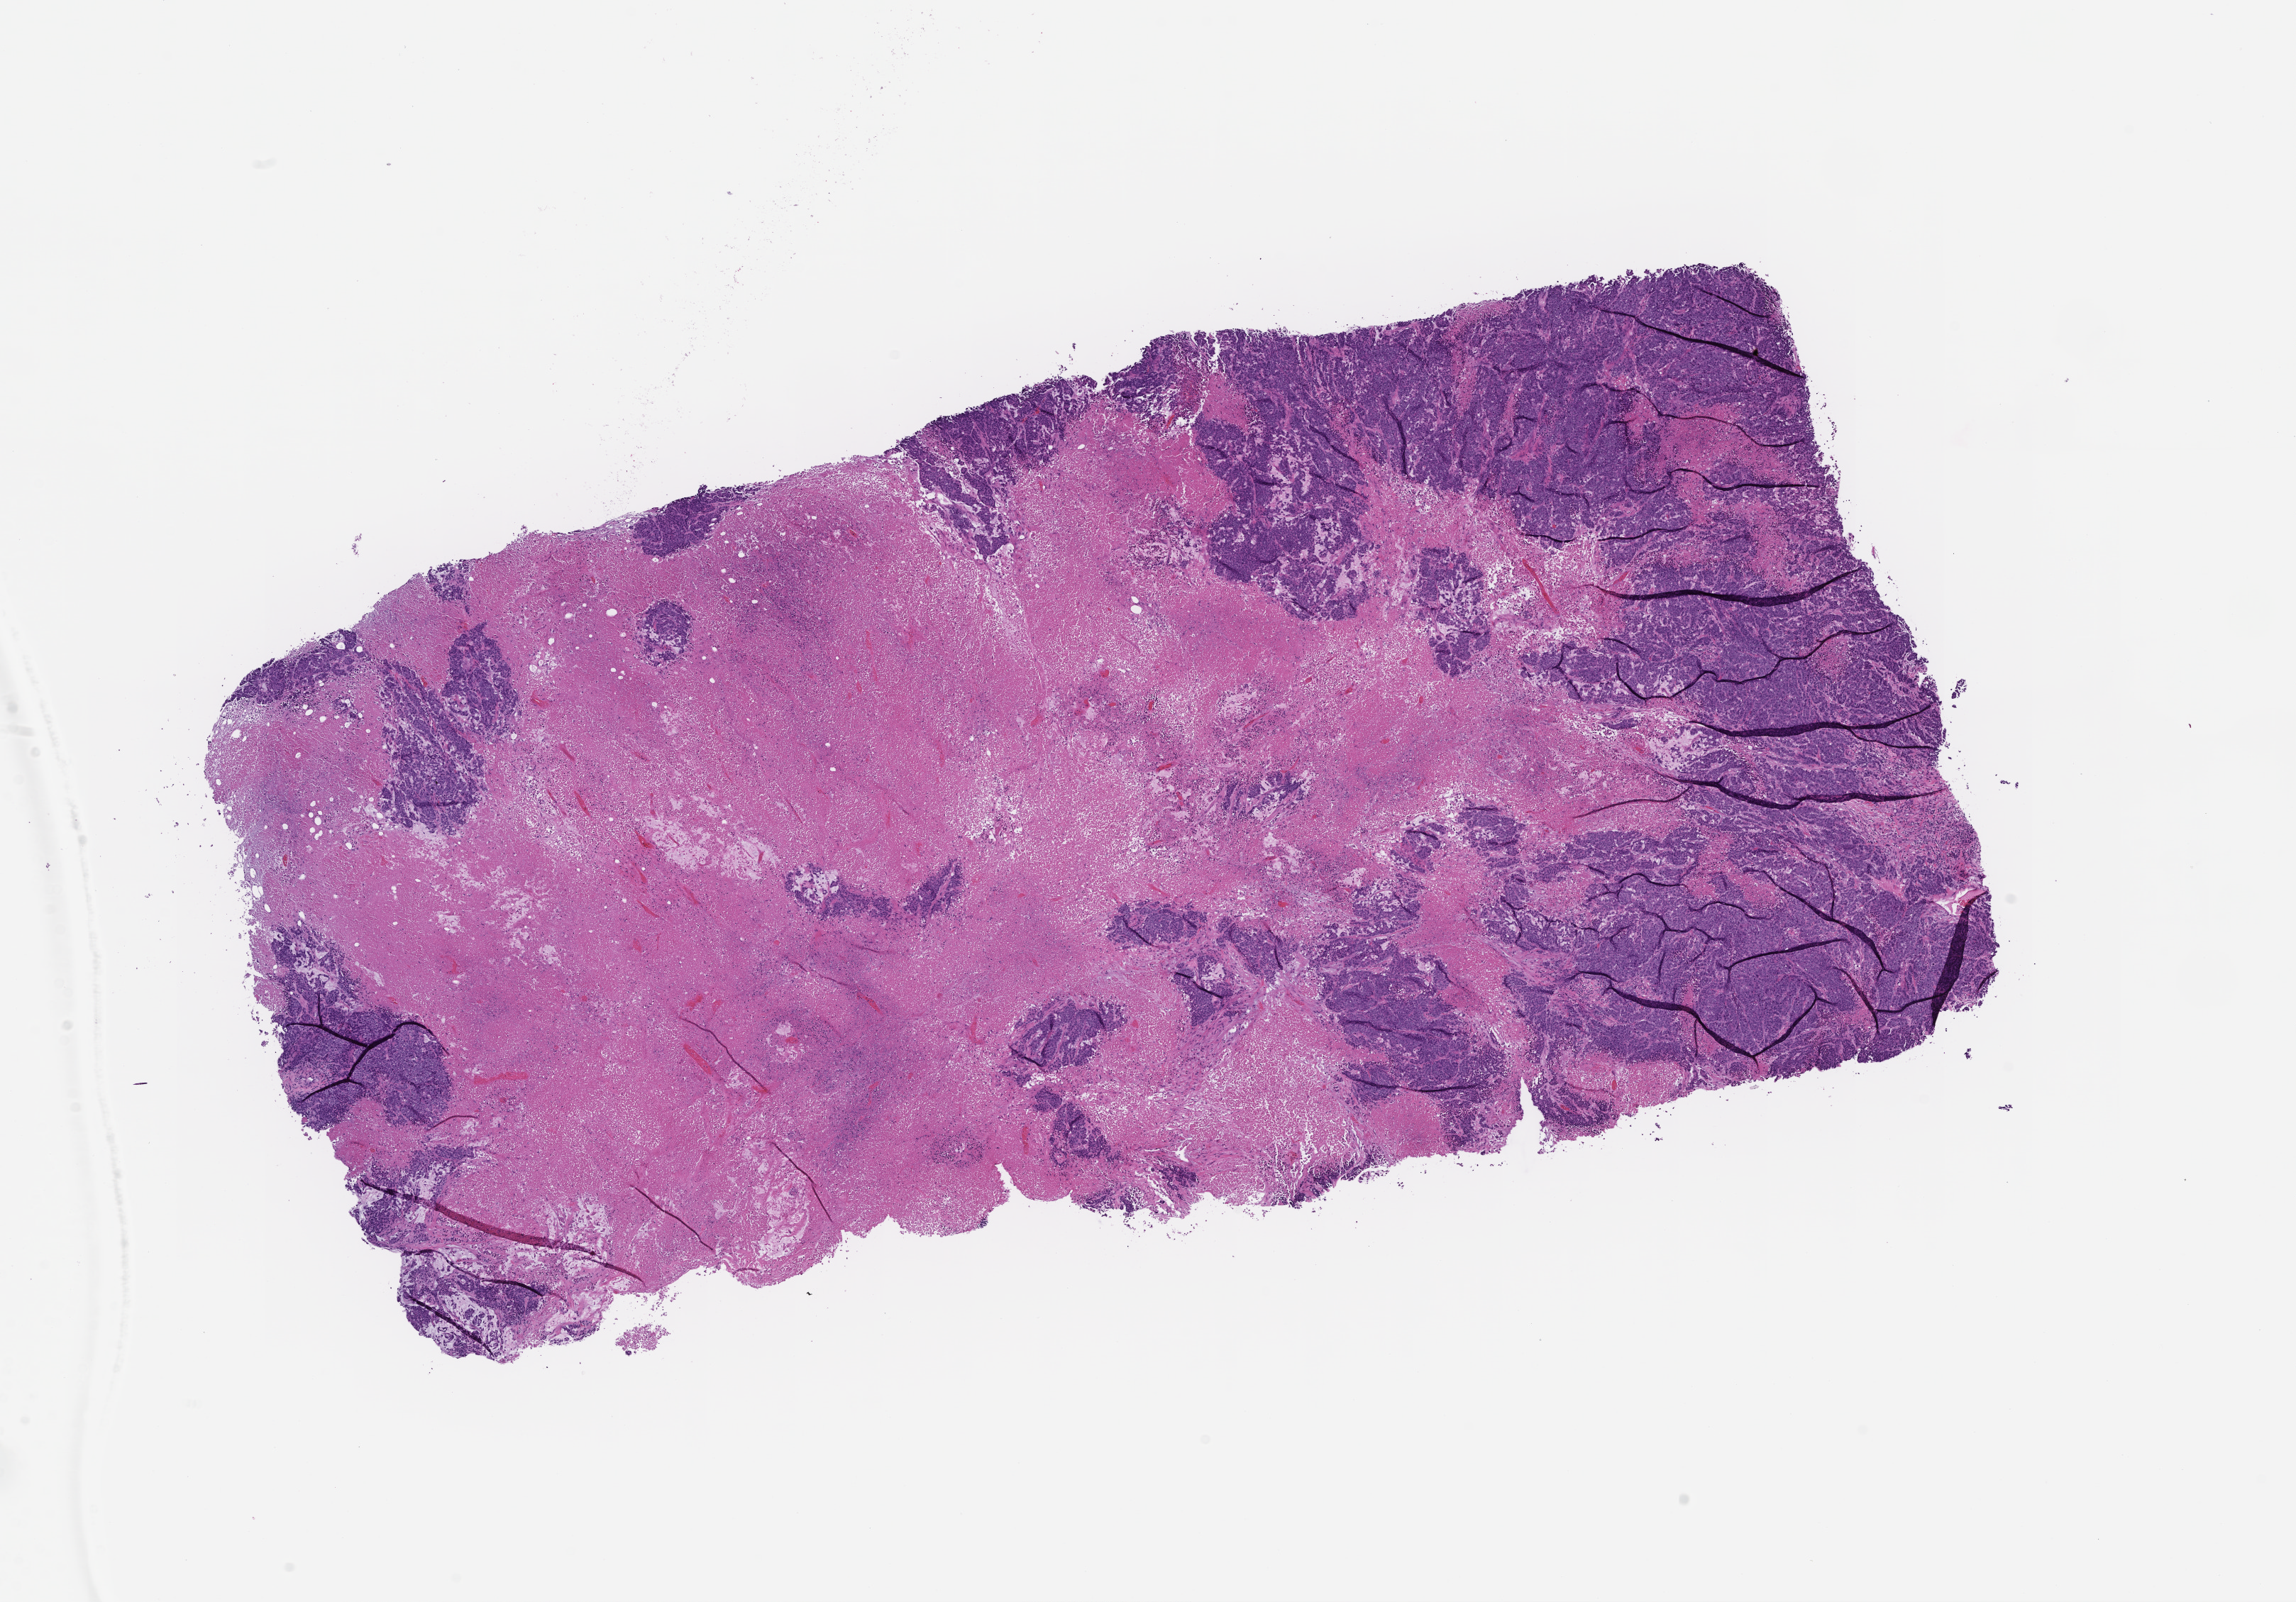
Whole-slide image, hematoxylin and eosin (H&E) stain — low-resolution overview of the scanned area, about 13.1 x 9.1 mm, formalin-fixed paraffin-embedded section, specimen time point: collected at baseline (before treatment). Patient sex: female.
This section: metastasis (sampled organ not recorded). Patient diagnosis (primary): Colorectal Carcinoma.